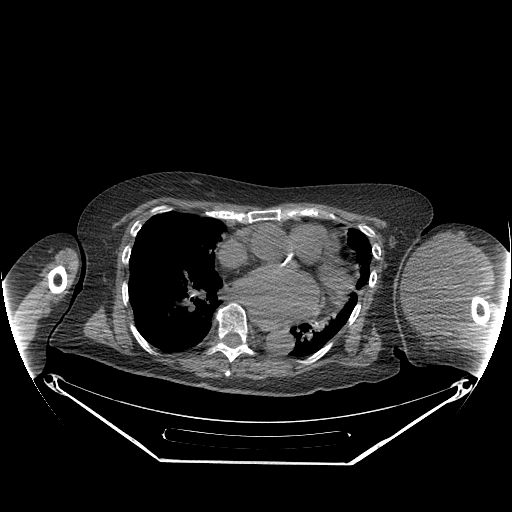
CT of an extremity soft-tissue mass (from a PET/CT study), one axial slice; slice 167 of 267 in the series (ordered by position); reconstruction kernel STANDARD; soft-tissue window (W 400 / L 40 HU); 512 × 512 image matrix. Female patient. Case-level facts recorded for this patient, not image findings: histological type: pleiomorphic leiomyosarcoma; grade: high; site of the primary tumour: left biceps.
Structures marked on this image (expert contour drawn on MRI and transferred to this co-registered scan by the dataset authors):
- gross tumour volume including surrounding oedema: bounding box <402,233,487,330> (left, top, right, bottom; pixels)
- gross tumour volume (mass): <402,233,481,328>